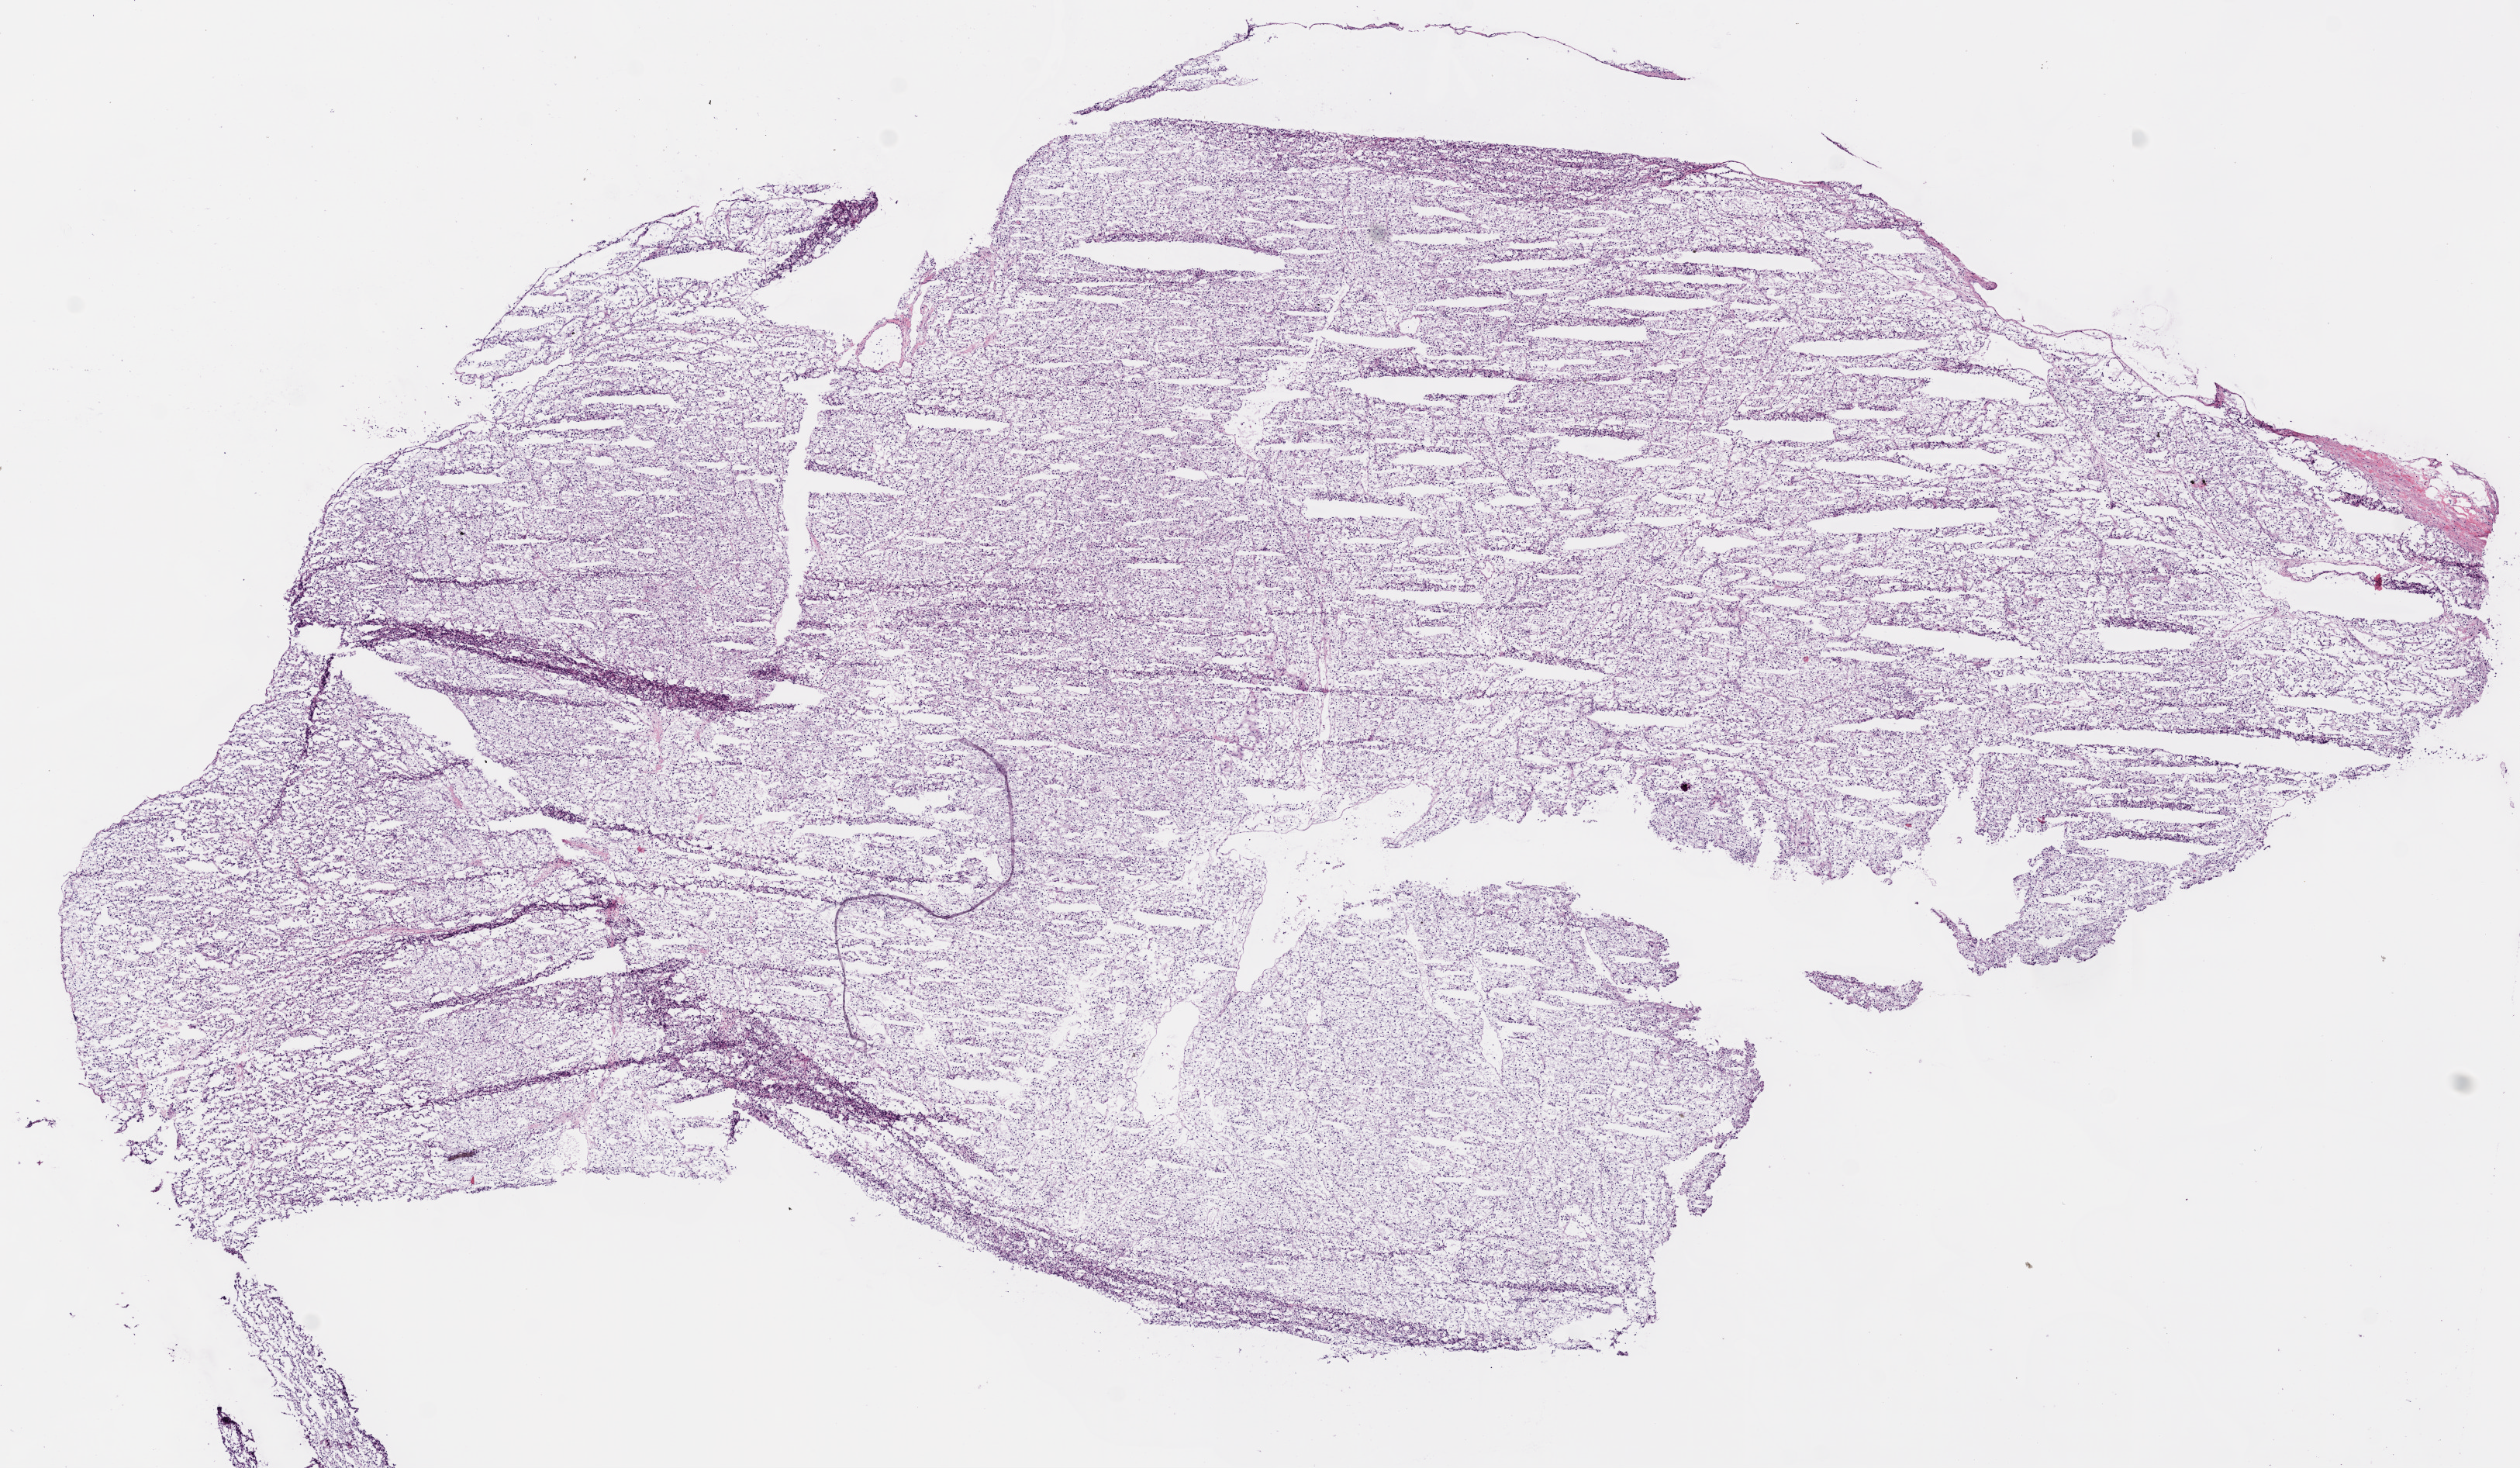
Hematoxylin and eosin (H&E) stained whole-slide image — a low-resolution overview of the entire scanned area, about 13.0 x 7.6 mm; frozen section; sample: primary tumour, kidney. Female patient; age at initial diagnosis 64 years. Histologic grade: G2 (moderately differentiated). Slide review estimates, as recorded: tumour cells 95%, tumour nuclei 90%, normal cells 0%, stromal cells 5%, necrosis 0%.
AJCC pathologic stage: I. TNM: T1b N0 M0. Pathologic diagnosis: Clear cell adenocarcinoma, NOS.